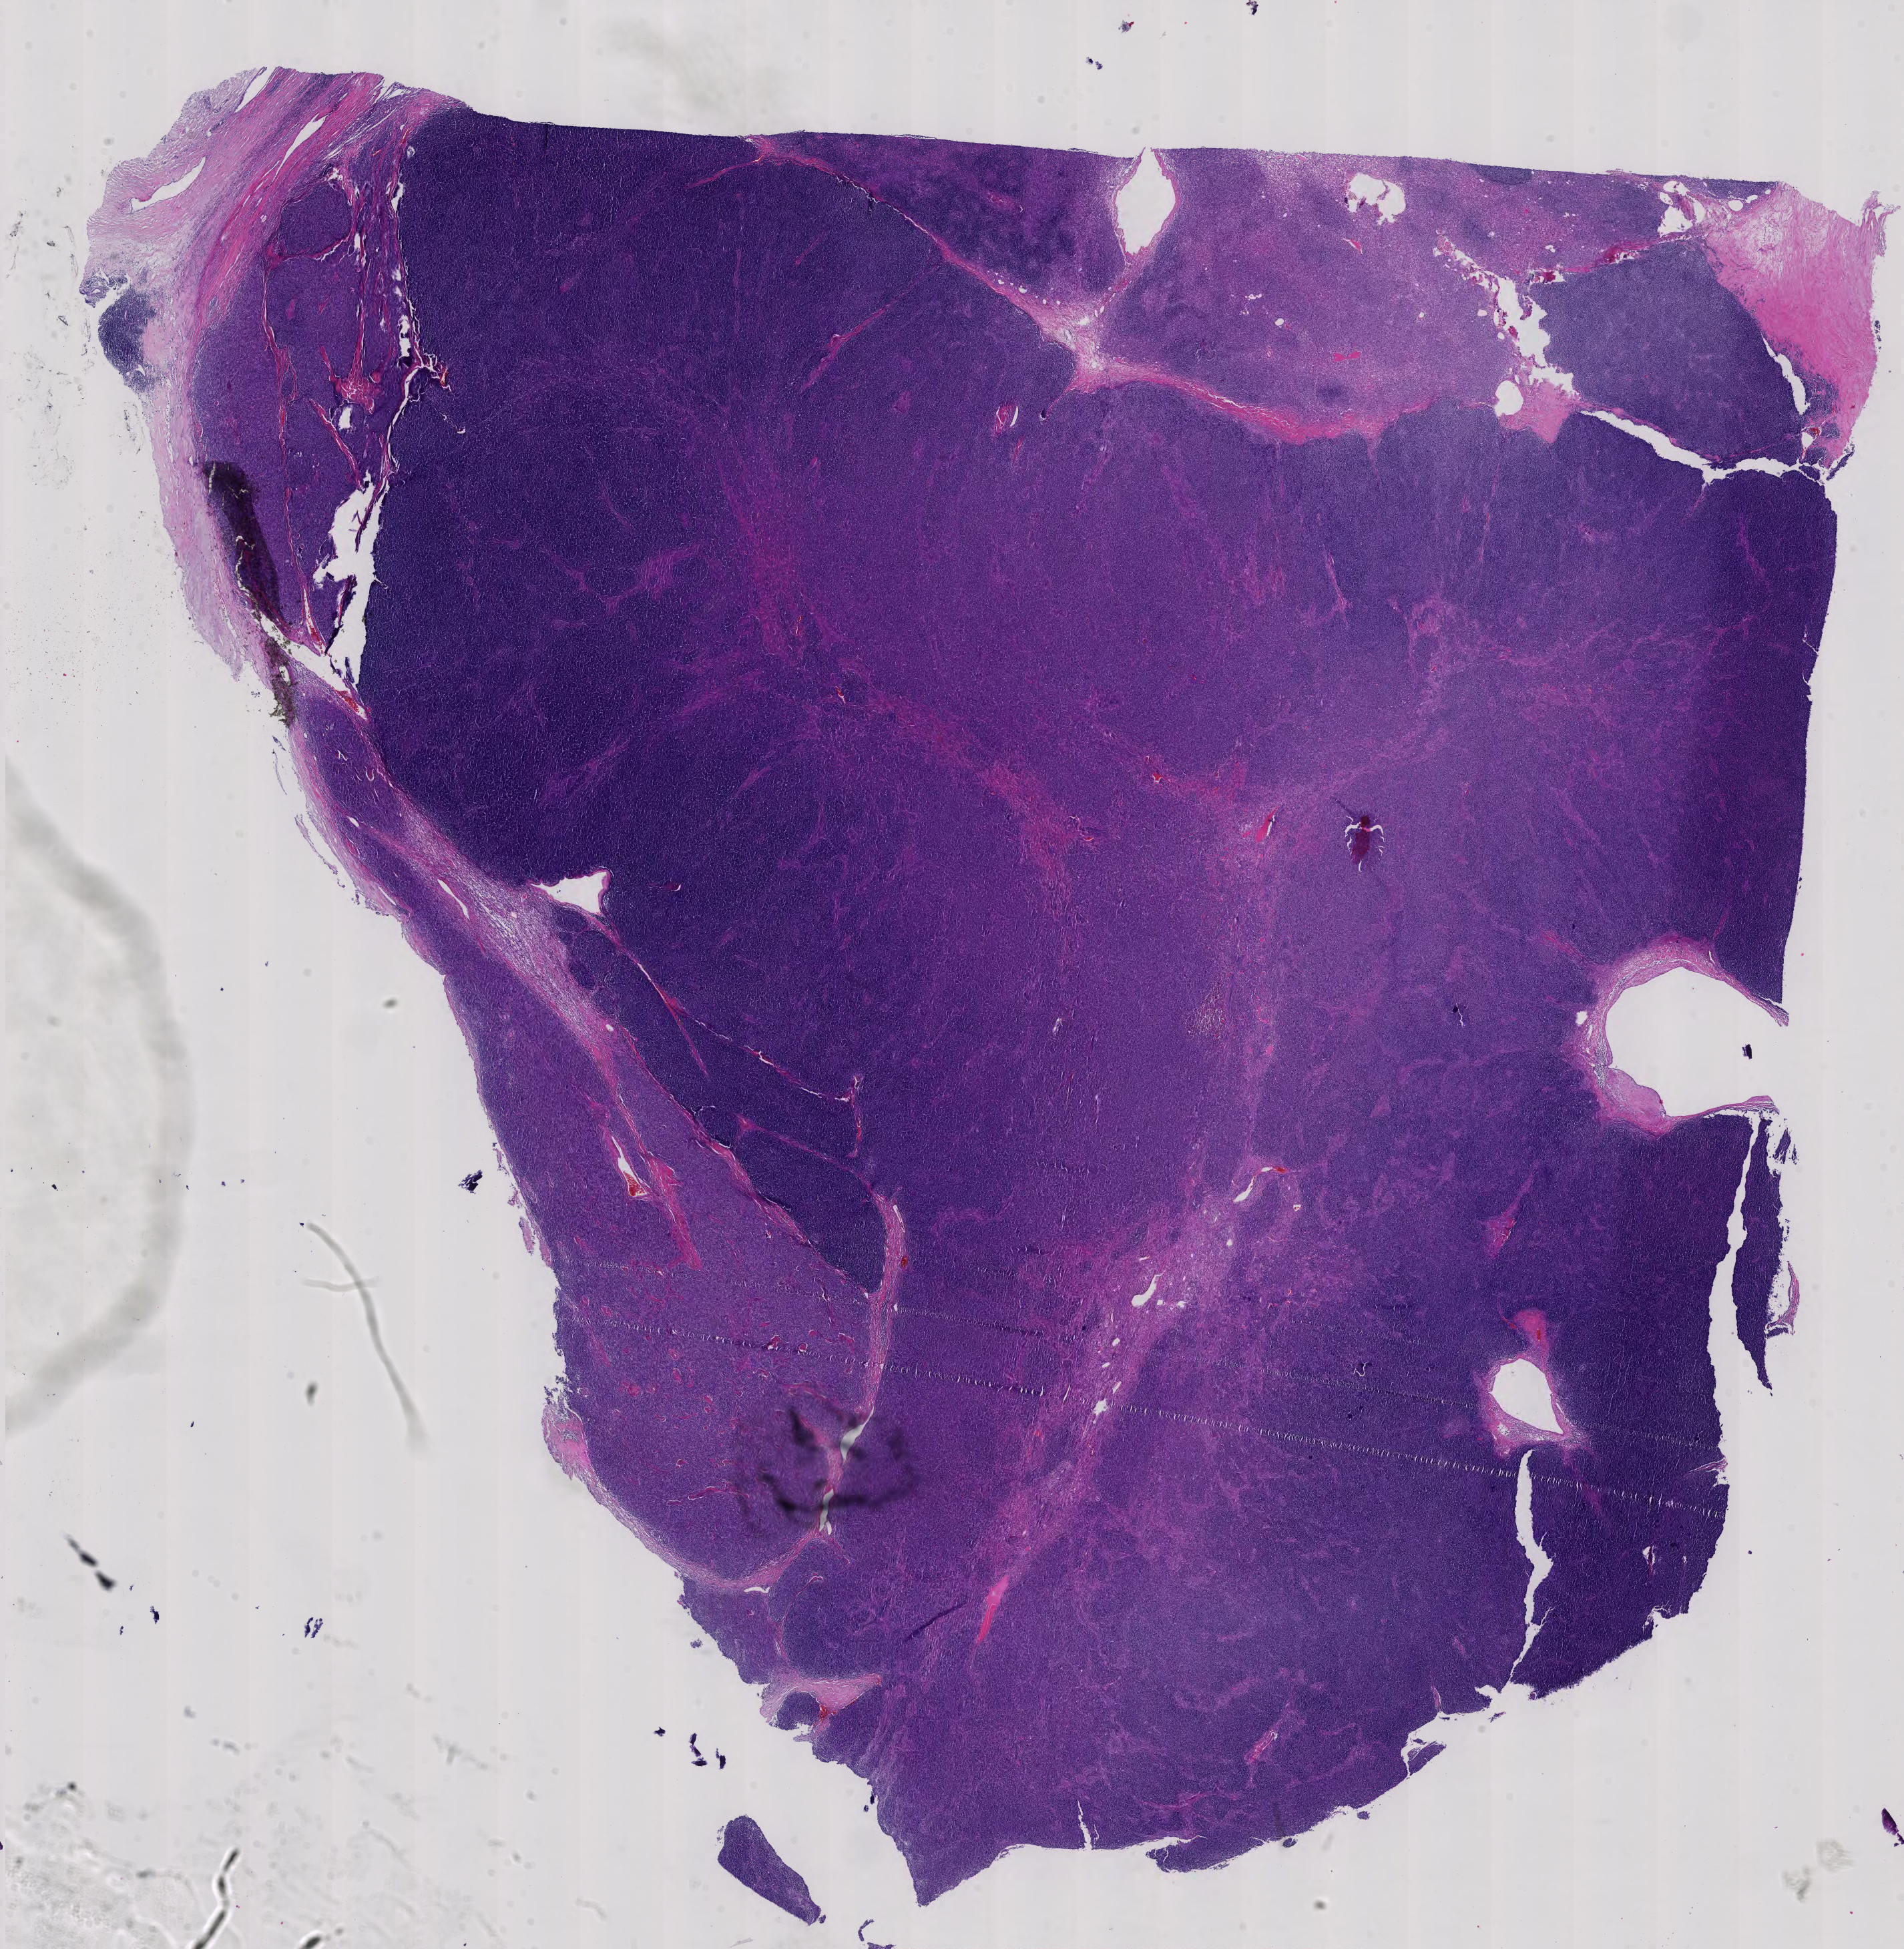
H&E-stained whole-slide image — whole scanned area (about 20.8 x 21.3 mm, slide scanned at 40x) shown as a low-resolution overview; formalin-fixed paraffin-embedded (FFPE) diagnostic section; sample: primary tumour, thymus. Female patient; age at initial diagnosis 52 years.
* diagnosis: Thymoma, type AB, malignant (anterior mediastinum)